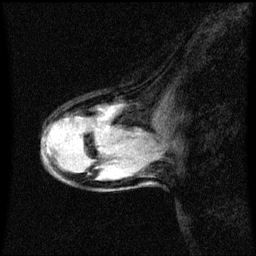
Breast MRI (dynamic contrast-enhanced), one sagittal slice. Position 30 of 60 along the scan axis. Dynamic contrast-enhanced series, image 2 of 3 at this slice position (ordered by acquisition). 1.5 T. TE 4.2 ms, TR 8.4 ms. 256 × 256 image matrix, field of view 200 × 200 mm. Female patient, age 38 years. From the clinical record (not read from this slice): setting: breast cancer imaged before/during neoadjuvant chemotherapy; receptor status: HR-positive, HER2-negative.
Outlined on this slice (semi-automatically segmented with operator editing):
- analysis volume of interest (the breast-tissue region the enhancement analysis was run in; not a lesion): box from (x=38, y=96) to (x=143, y=189) px
- tumour enhancement mask (voxels above the 70 % enhancement threshold inside the analysis volume of interest): (x=105, y=116)–(x=108, y=119)